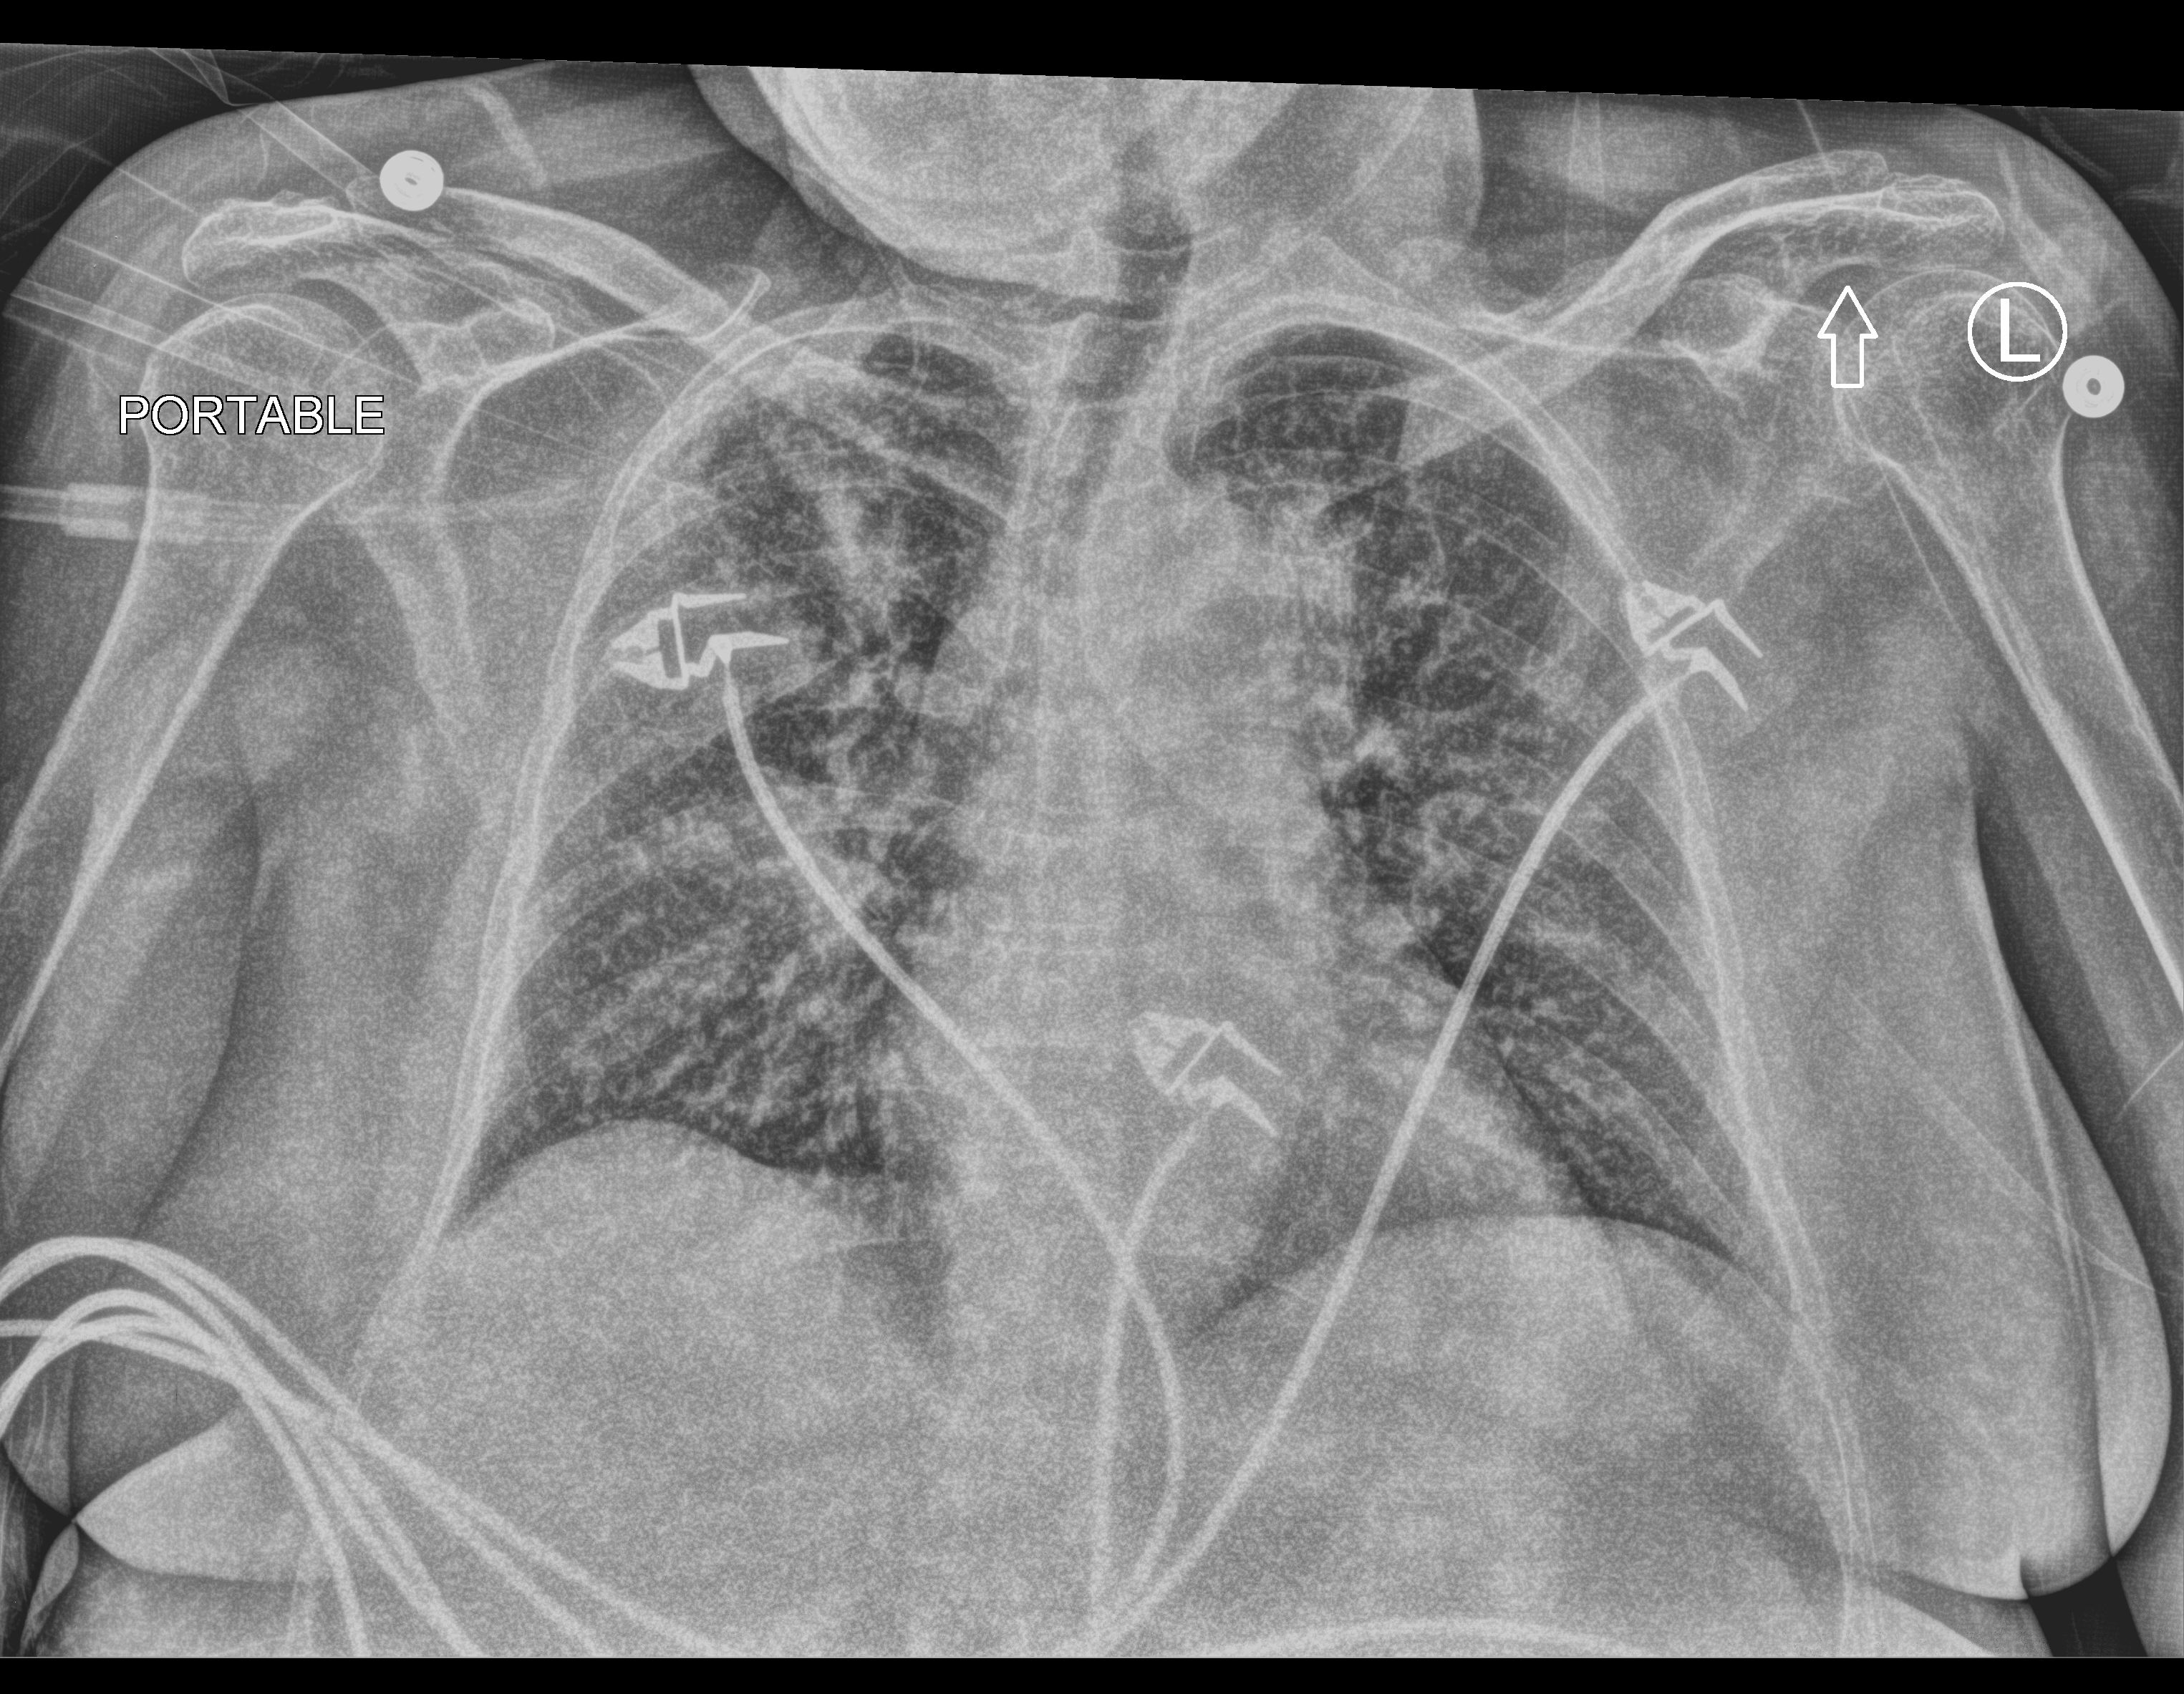
Bedside chest radiograph (computed radiography). Patient hospitalised with COVID-19; female, aged 18–59 years.
Admission-level facts for this patient (not findings on this image; timing relative to this image not recorded):
- admitted to intensive care during this hospital stay: no
- mechanically ventilated during this hospital stay: no
- length of hospital stay: 20 days